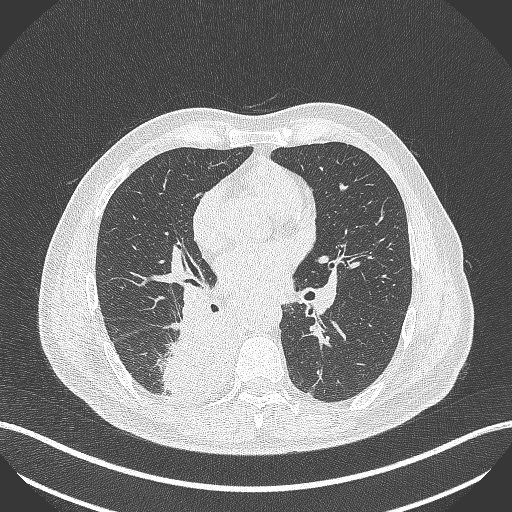
Chest CT, one axial slice. Slice 241 of 451 in the series (ordered by position). Reconstruction kernel B70f. Lung window (W 1500 / L -600 HU). 512 × 512 image matrix, field of view 400 × 400 mm. Male patient, age 61 years. From the clinical record (not read from this slice): clinical TNM (as recorded): T1 N0 M0; histopathological grade: G3.
Structures marked on this image (rectangle marked by the reading radiologist):
- lung tumour (recorded histology: small cell carcinoma): bounding box (x1, y1, x2, y2) in pixels: (158, 311, 232, 398)